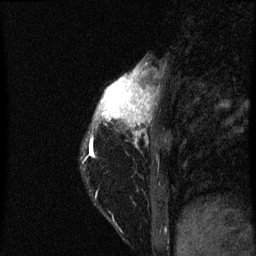
Breast MRI (dynamic contrast-enhanced), one sagittal slice; slice 15 of 60 in the series (ordered by position); dynamic contrast-enhanced series, image 2 of 3 at this slice position (ordered by acquisition); 1.5 T; TE 4.2 ms, TR 8 ms; 2 mm slice thickness; 256 × 256 image matrix, field of view 180 × 180 mm. Patient: female, 38 years.
Annotated regions visible in this slice (semi-automatically segmented with operator editing):
- analysis volume of interest (the breast-tissue region the enhancement analysis was run in; not a lesion): bounding box [x1, y1, x2, y2] px = [86, 68, 157, 147]
- tumour enhancement mask (voxels above the 70 % enhancement threshold inside the analysis volume of interest): [98, 70, 151, 127]